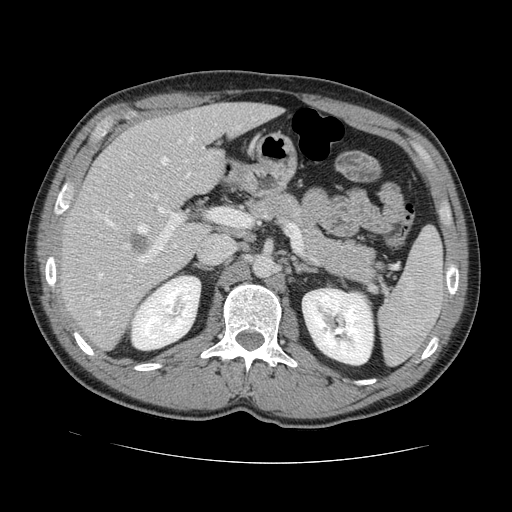
Contrast-enhanced abdominal CT, one axial slice. Position 78 of 131 along the scan axis. 120 kVp. Soft-tissue window (W 400 / L 40 HU). 512 × 512 image matrix, field of view 380 × 380 mm. Male patient, age 40 years. Case-level facts recorded for this patient, not image findings: diagnosis: colorectal cancer liver metastases, imaged before liver resection; multiple liver metastases: yes; largest metastasis: 2.9 cm; disease in both lobes: yes.
Structures marked on this image (manually delineated by an expert):
- hepatic veins: bounding box (x1, y1, x2, y2) in pixels: (97, 137, 191, 315)
- liver: (62, 104, 277, 348)
- planned liver remnant (the part of the liver to remain after resection): (106, 104, 277, 199)
- portal vein (with intrahepatic branches): (137, 193, 234, 267)
- liver metastasis: (130, 233, 151, 255)